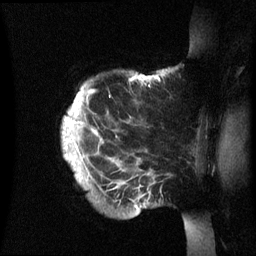
Breast MRI (dynamic contrast-enhanced), one sagittal slice. Slice 53 of 60 in the series (ordered by position). Dynamic contrast-enhanced series, image 2 of 3 at this slice position (ordered by acquisition). 1.5 T. TE 4.2 ms, TR 8.4 ms. 256 × 256 image matrix, field of view 230 × 230 mm. Patient: female, 48 years.
Structures marked on this image (semi-automatic segmentation, software-assisted and operator-edited):
- analysis volume of interest (the breast-tissue region the enhancement analysis was run in; not a lesion): bounding box <62,73,197,236> (left, top, right, bottom; pixels)
- tumour enhancement mask (voxels above the 70 % enhancement threshold inside the analysis volume of interest): <63,75,149,171>